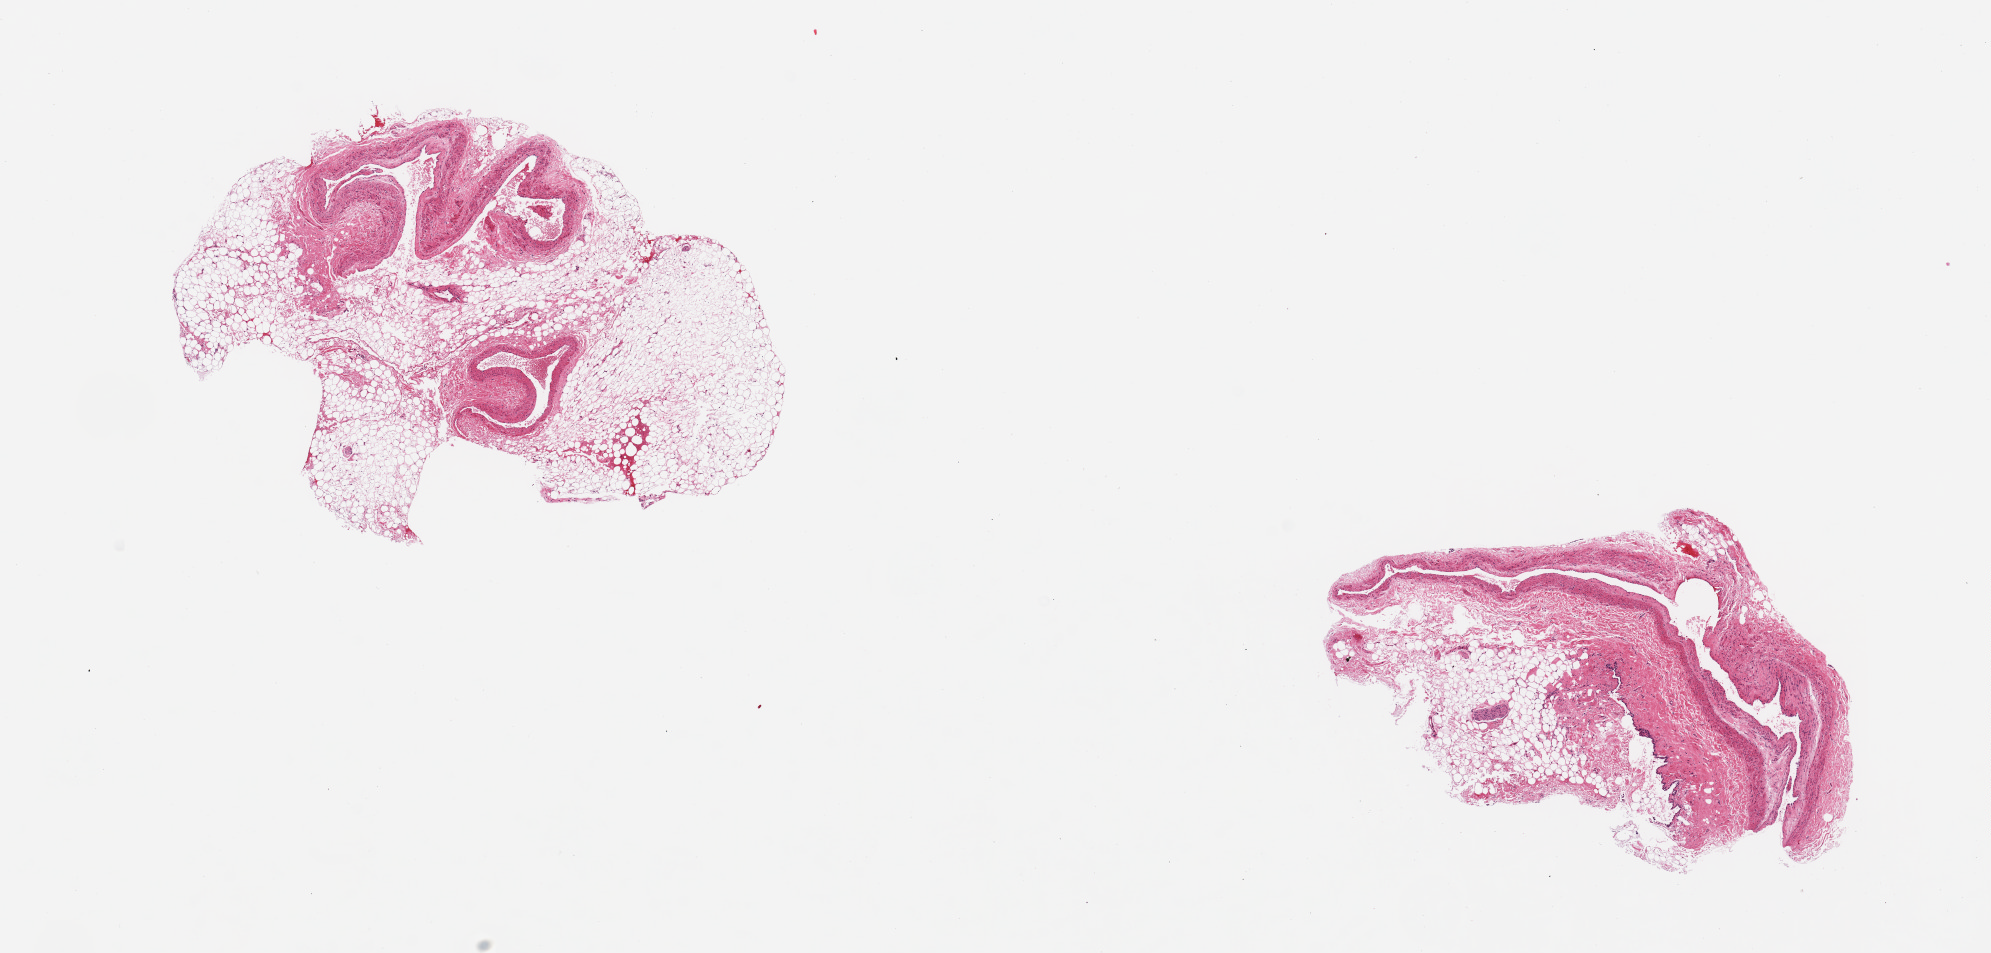
Digitized hematoxylin and eosin (H&E)-stained section, a low-resolution overview of the entire scanned area, about 15.8 x 7.5 mm. PAXgene-fixed paraffin-embedded (PFPE) section. Section of coronary artery (target tissue). Tissue donor sample. Donor sex: female.
Reviewer comment on this tissue sample: 2 pieces; several arteries and veins with 50% external fat; no plaques.